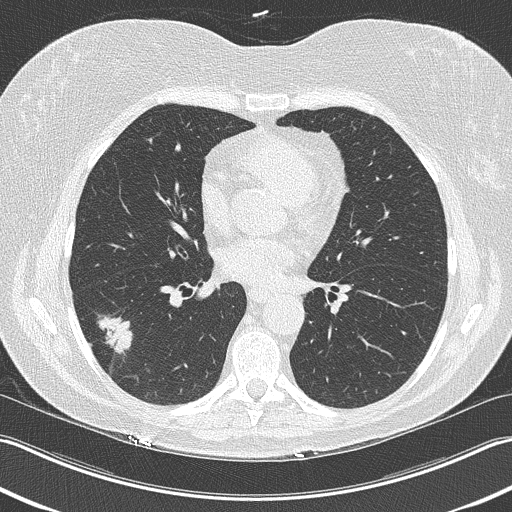
Low-dose screening chest CT, one axial slice; position 112 of 210 along the scan axis; reconstruction kernel B50f; 120 kVp; lung window (W 1500 / L -600 HU); 2 mm slice thickness; 512 × 512 image matrix, field of view 348 × 348 mm.
Outlined on this slice (expert manual segmentation):
- lesion 1 (tumor, lower lobe of right lung): bounding box [x1, y1, x2, y2] px = [97, 315, 133, 356]